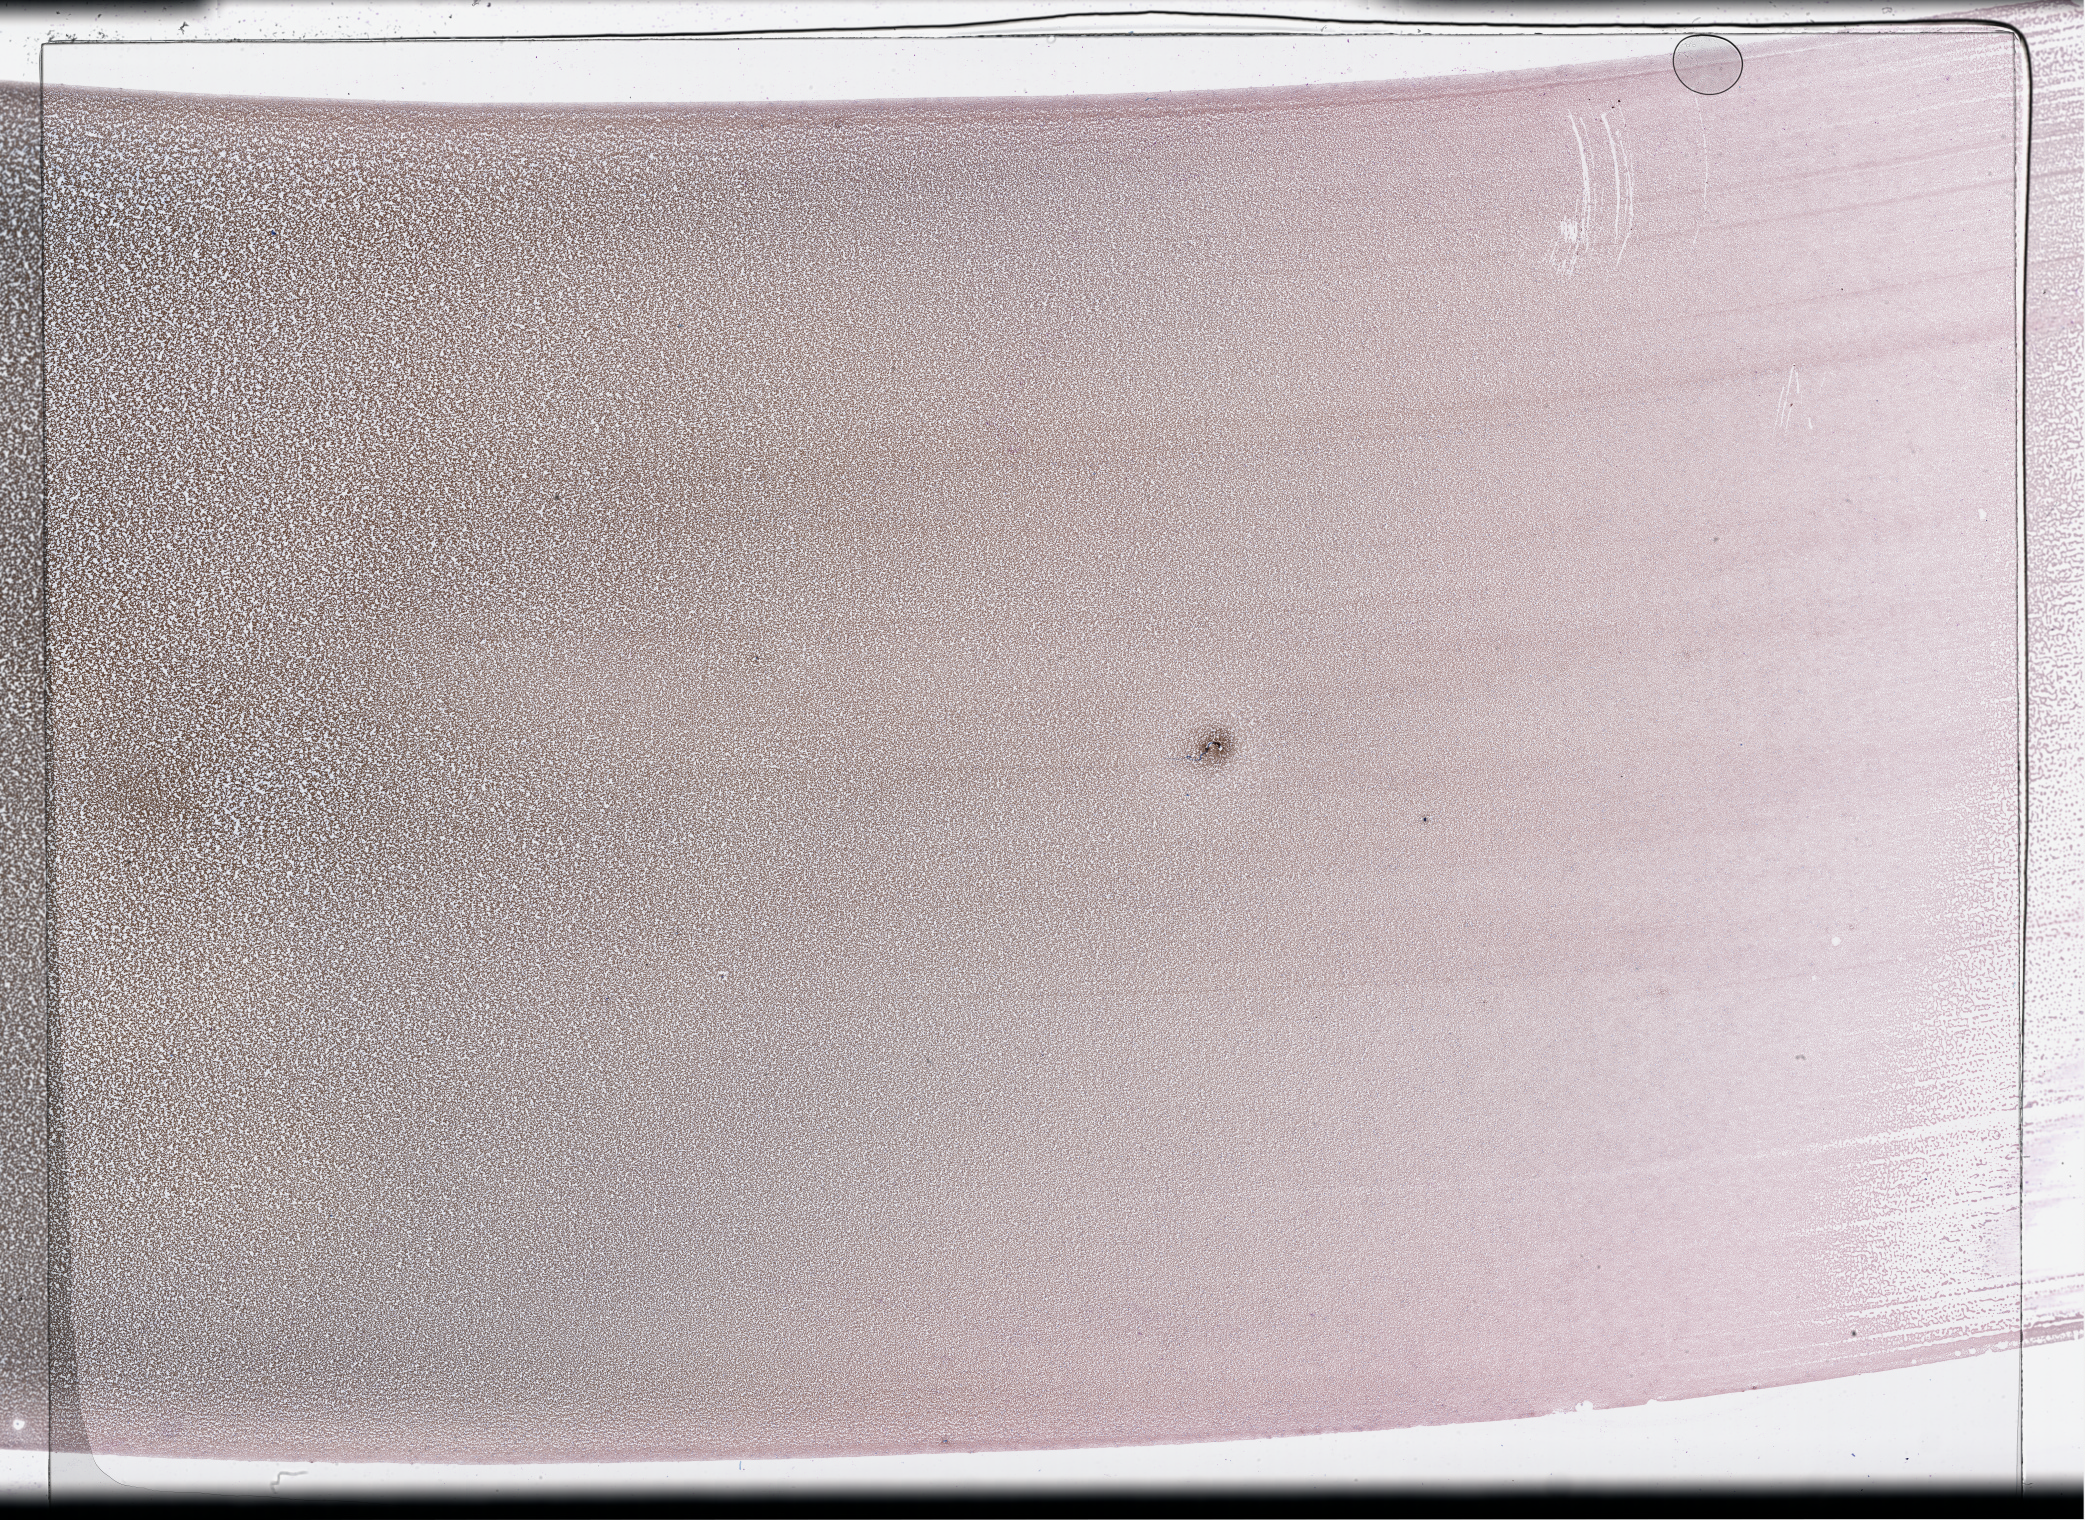
Whole-slide histology image, H&E-stained, whole scanned area (about 33.7 x 24.5 mm, acquisition: 40x scan) shown as a low-resolution overview. Peripheral blood (leukaemic) sample. Patient: male, age 69 years.
FAB classification: M2. Diagnosis: Acute Myeloid Leukemia.